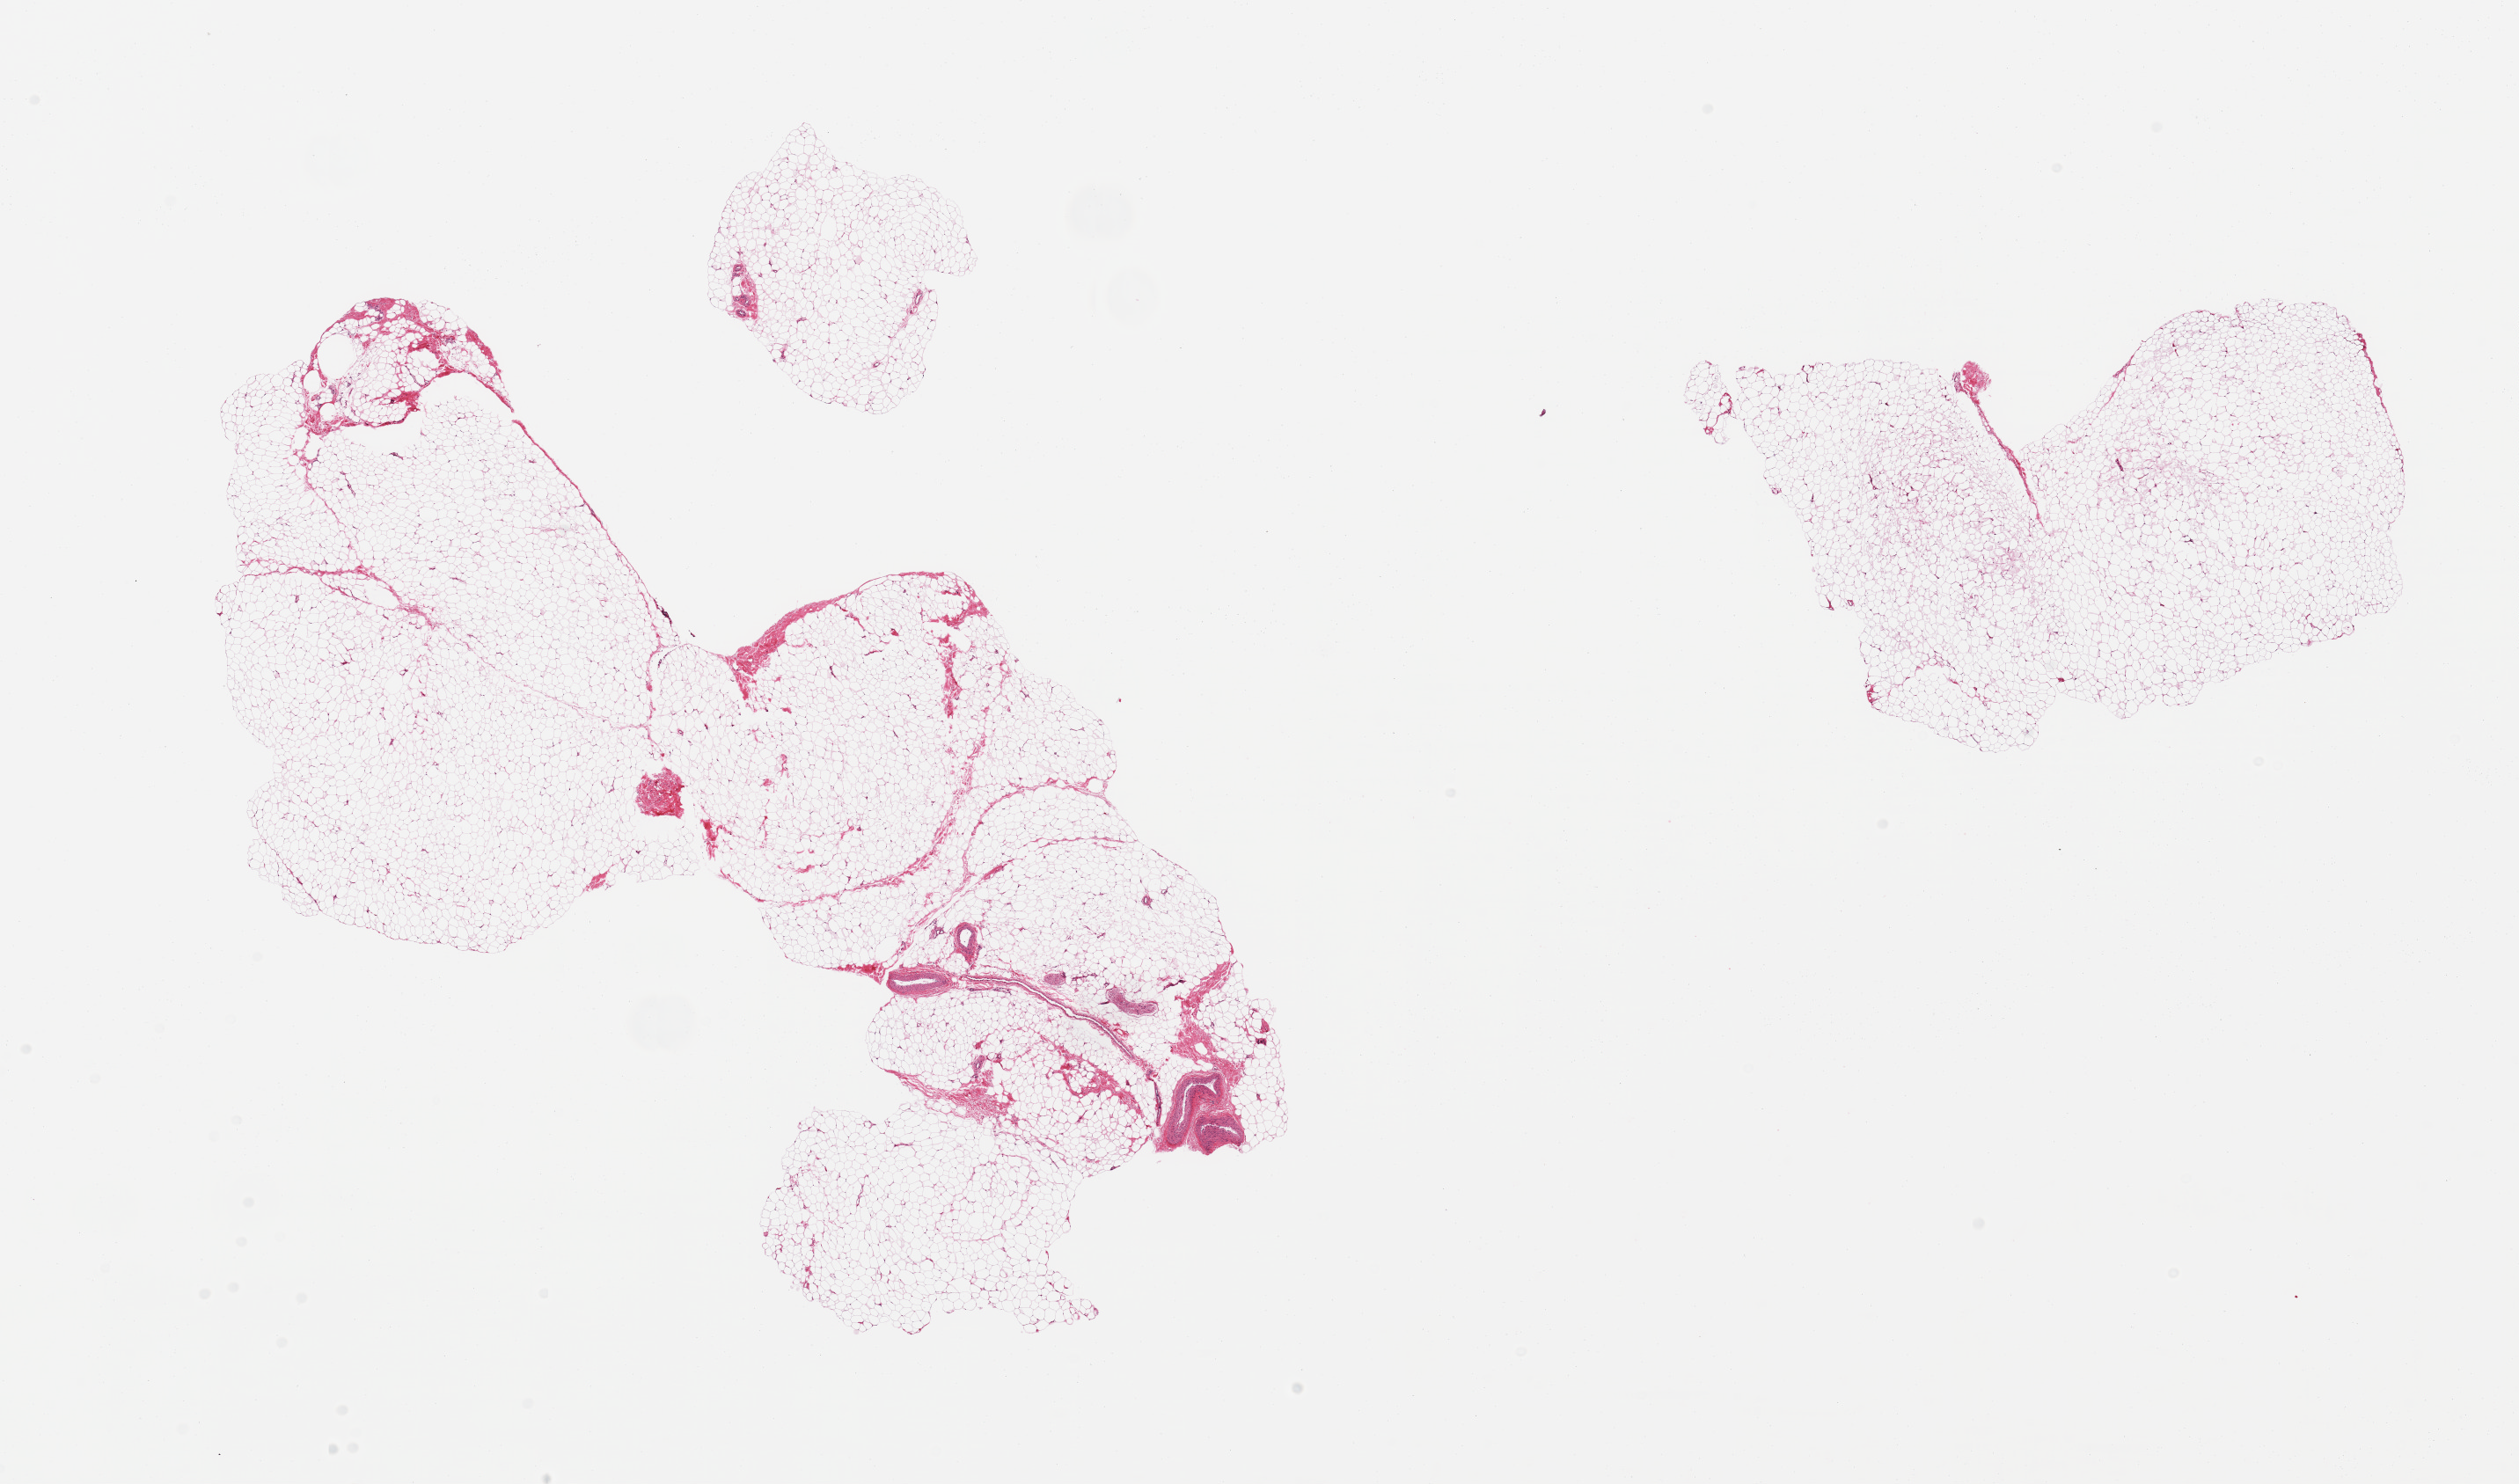
Whole-slide image, haematoxylin and eosin stain — low-resolution overview of the scanned area, about 22.6 x 13.3 mm (acquisition: 20x scan). PAXgene-fixed, paraffin-embedded tissue. Section of breast (target tissue). Donor tissue sample. Donor sex: male.
Review note (as recorded): 2 pieces, fibroadipose elements only.